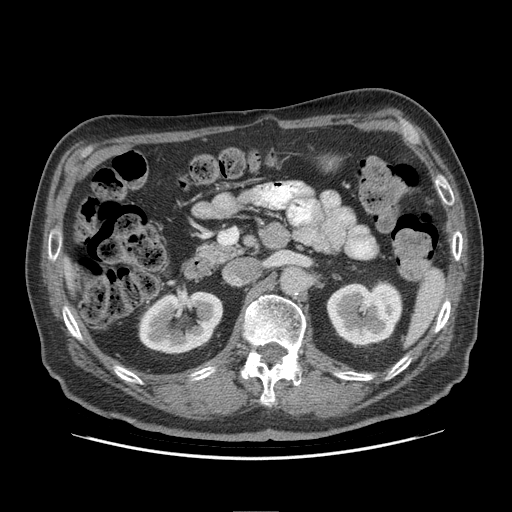
Contrast-enhanced abdominal CT (liver protocol), one axial slice. Position 43 of 95 along the scan axis. Soft-tissue window (W 400 / L 40 HU). 512 × 512 image matrix, field of view 400 × 400 mm. Case-level facts recorded for this patient, not image findings: diagnosis: hepatocellular carcinoma (patient treated with transarterial chemoembolisation; whether this scan precedes or follows treatment is not stated here); TNM stage (as recorded): Stage-IVB; Child-Pugh class: A; tumour differentiation: well differentiated.
Outlined on this slice (semi-automatic segmentation, software-assisted and operator-edited):
- liver parenchyma outside the tumour (the mass and vessels are separate outlines, so this box may not span the whole liver): box from (x=62, y=256) to (x=76, y=292) px